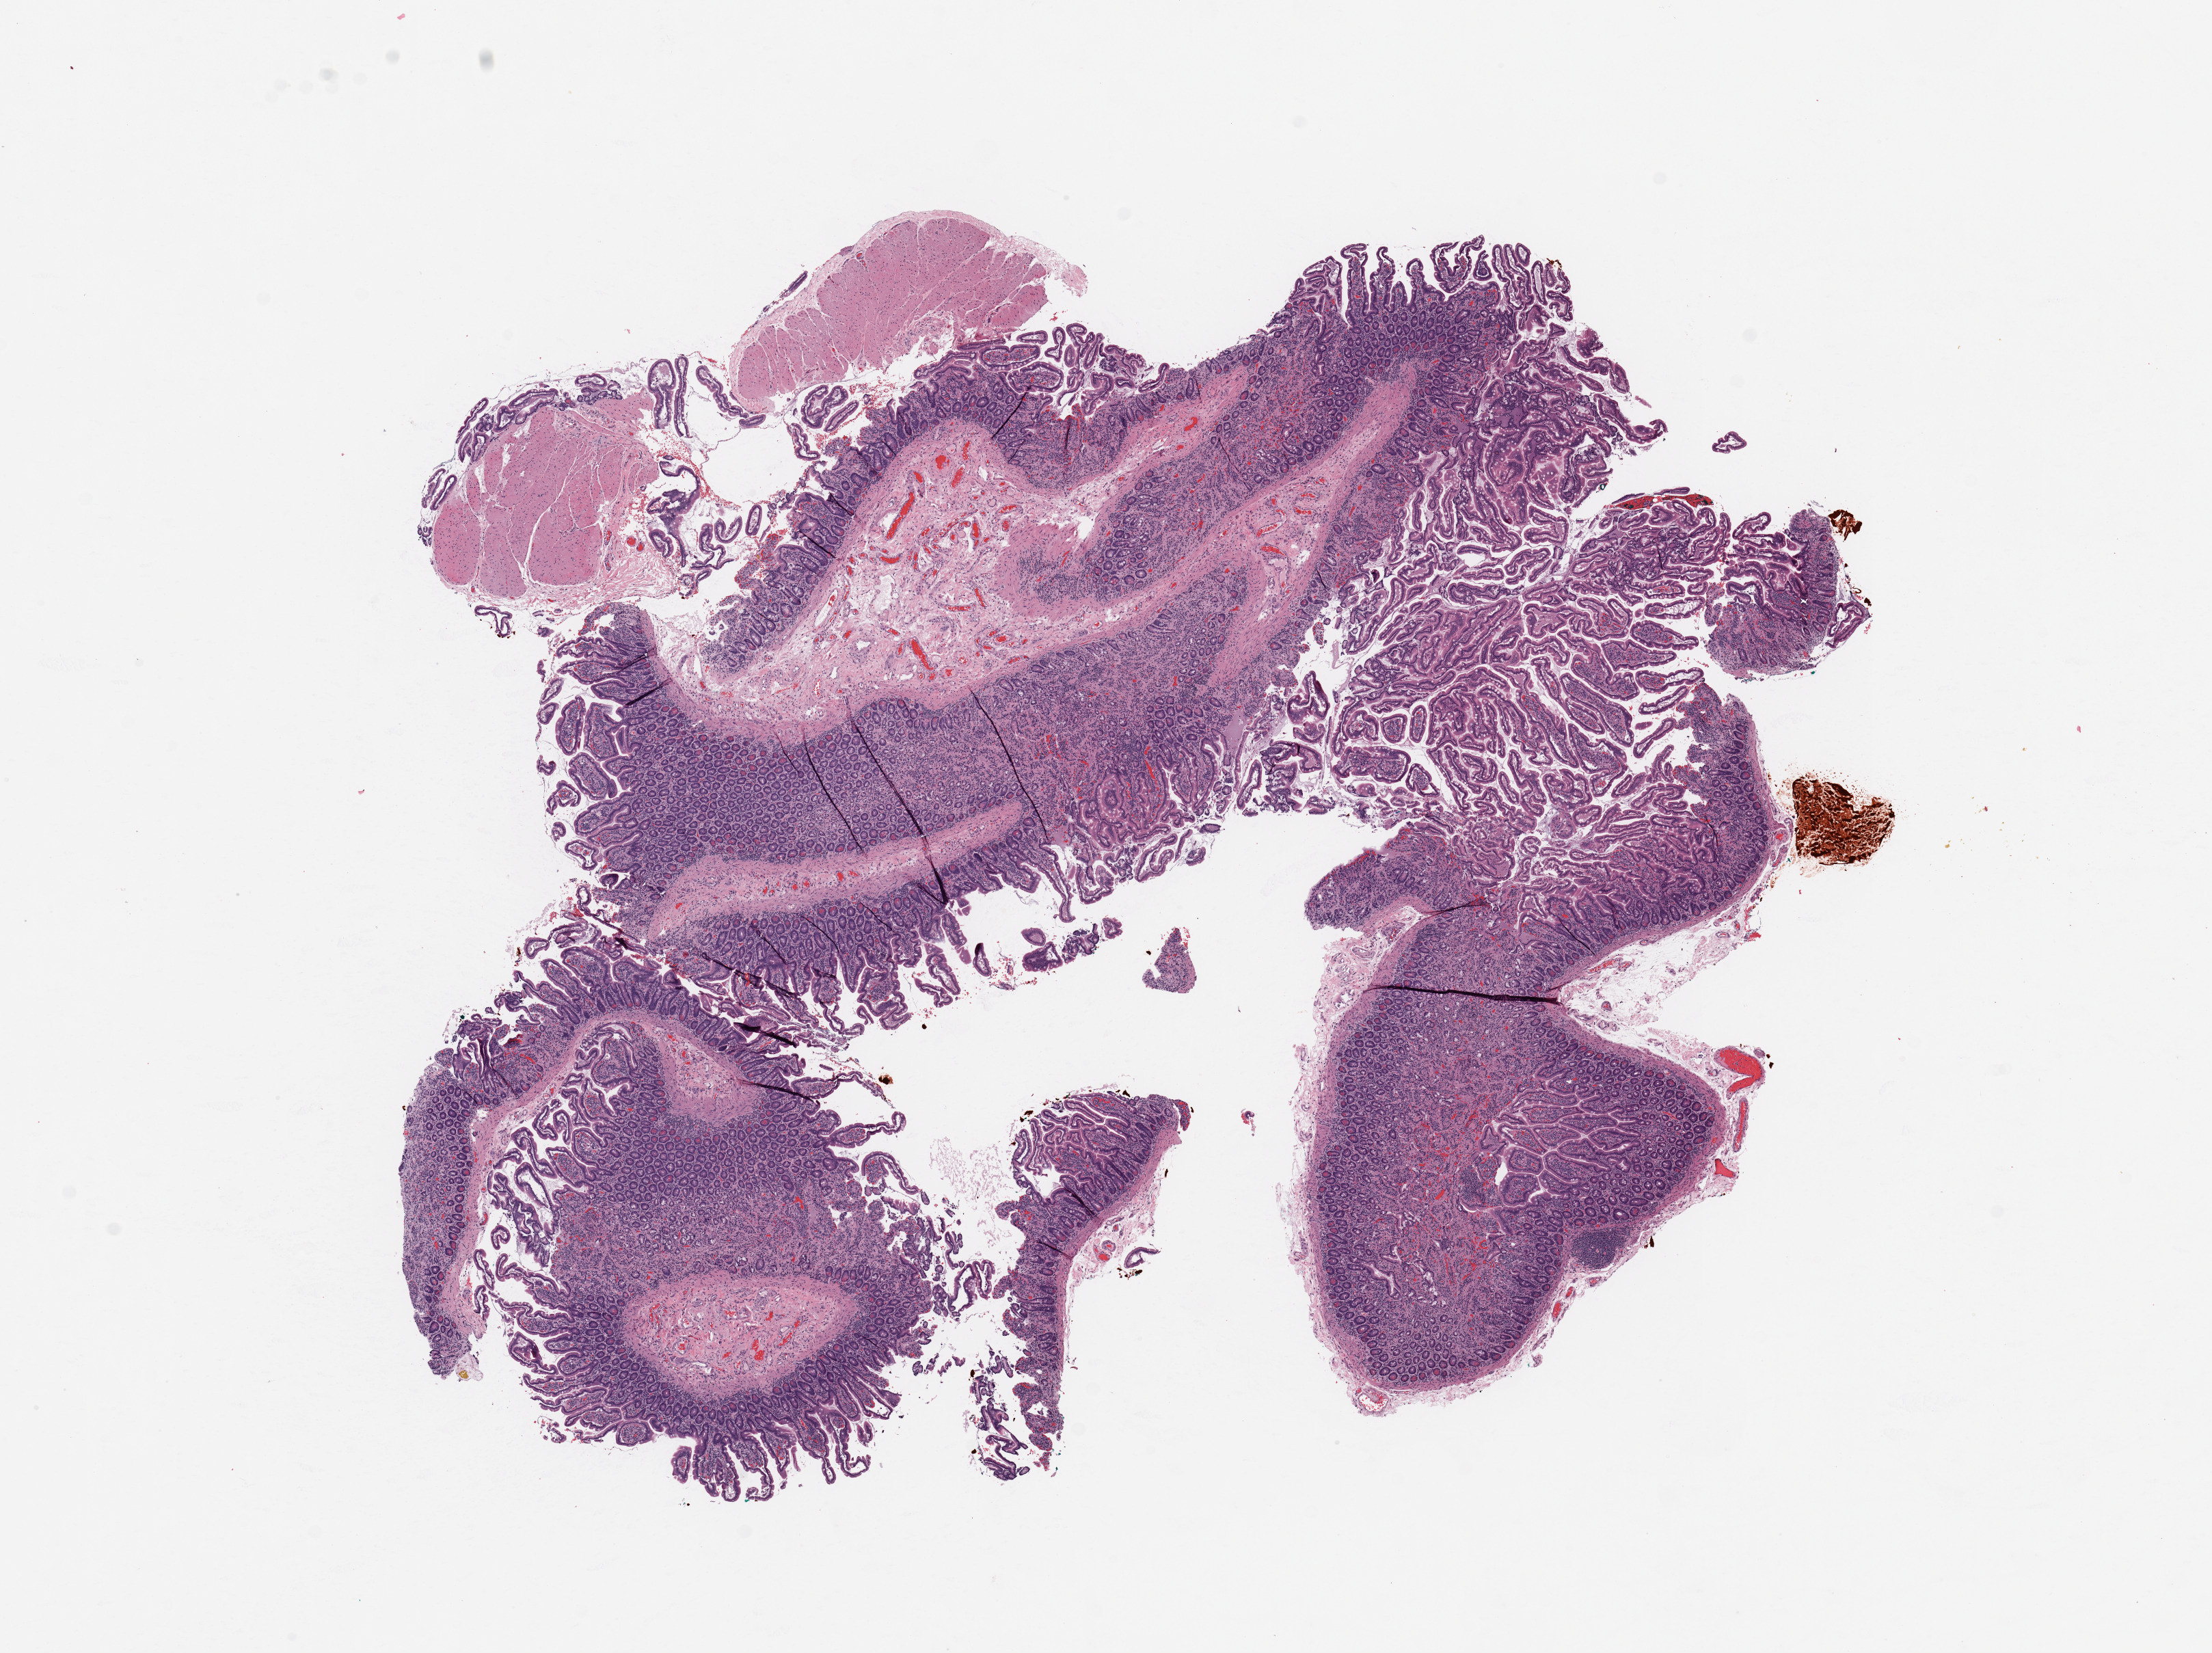
Digitized H&E-stained tissue section (whole slide) — a low-resolution overview of the entire scanned area, about 12.8 x 9.6 mm (acquisition: 20x scan). Normal (non-tumour) tissue sample, sampled site: pancreas. Patient: male, age 70 years.
• this section: normal (non-tumour) tissue from the same patient
• patient diagnosis: Infiltrating duct carcinoma, NOS